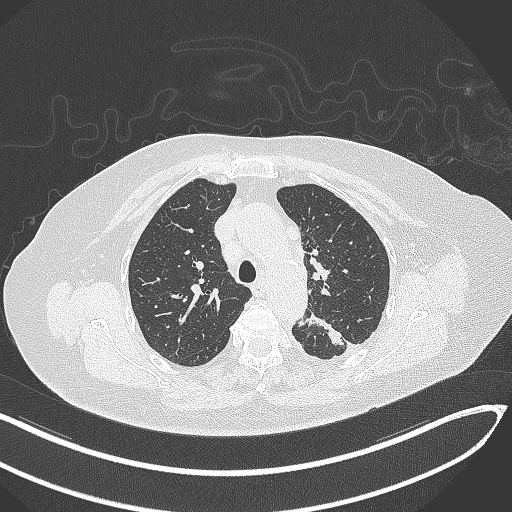
Chest CT, one axial slice; slice 226 of 270 in the series (ordered by position); lung window (W 1500 / L -600 HU); 1 mm slice thickness; 512 × 512 image matrix, field of view 400 × 400 mm. Female patient, age 76 years. Case-level facts recorded for this patient, not image findings: clinical TNM (as recorded): T1c N0 M0.
Structures marked on this image (bounding box drawn by a radiologist):
- lung tumour (recorded histology: adenocarcinoma): bounding box [x1, y1, x2, y2] px = [296, 310, 345, 350]